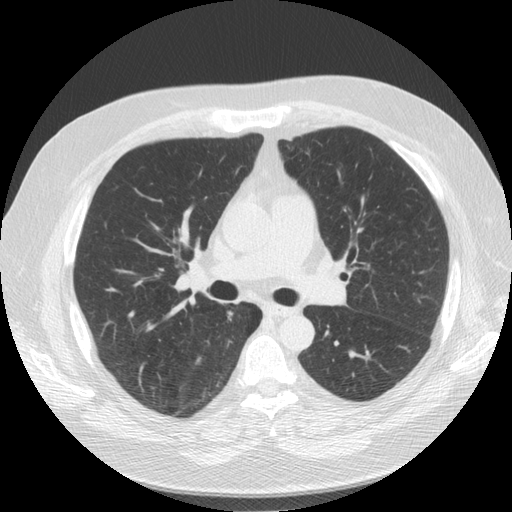
Low-dose screening chest CT, one axial slice; lung window (W 1500 / L -600 HU); 2.5 mm slice thickness; 512 × 512 image matrix.
Structures marked on this image (expert manual segmentation):
- lesion 1 (tumor, upper lobe of right lung): bounding box <226,309,235,319> (left, top, right, bottom; pixels)